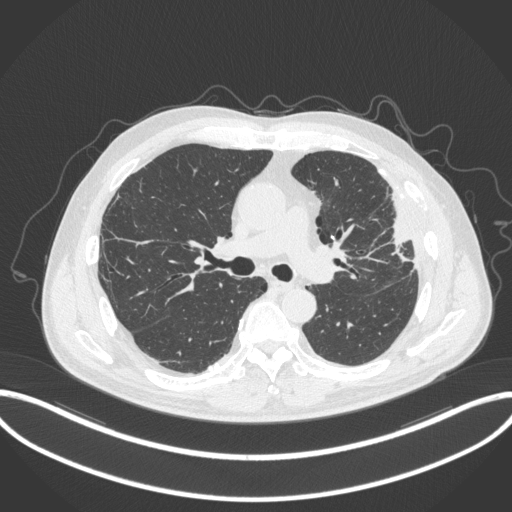
Chest CT, one axial slice. Slice 207 of 382 in the series (ordered by position). Reconstruction kernel B31f. Lung window (W 1500 / L -600 HU). 1 mm slice thickness. 512 × 512 image matrix, field of view 415 × 415 mm. Patient: male, 64 years. Case-level facts recorded for this patient, not image findings: clinical TNM (as recorded): T4 N1 M0; histopathological grade: G3.
Annotated regions visible in this slice (bounding box drawn by a radiologist):
- lung tumour (recorded histology: adenocarcinoma): bounding box <380,183,415,264> (left, top, right, bottom; pixels)